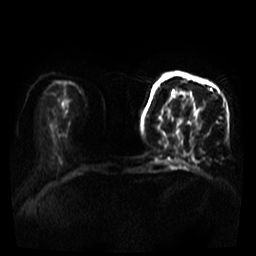
Breast MRI, one axial slice; slice 11 of 39 in the series (ordered by position); diffusion-weighted series; image 2 of 4 stored at this slice position (different b-values; order by instance number); 3 T; 5 mm slice thickness; 256 × 256 image matrix, field of view 320 × 320 mm. Female patient.
Outlined on this slice (expert manual segmentation):
- tumour on diffusion-weighted imaging: bounding box <164,142,167,145> (left, top, right, bottom; pixels)